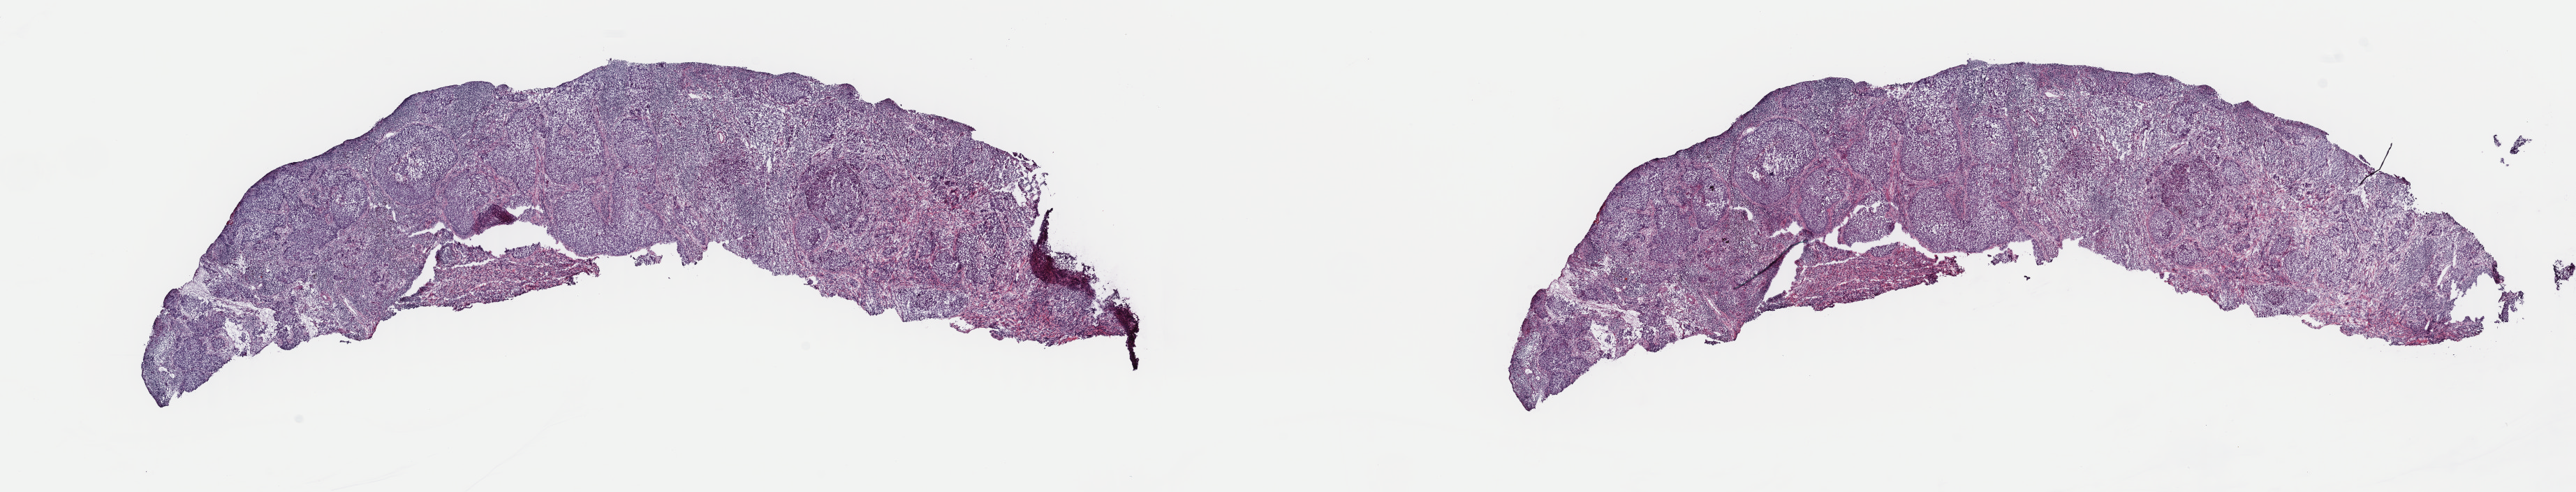
Digitized H&E tissue section (whole slide), whole scanned area (about 29.1 x 5.6 mm, from a 40x scan) shown as a low-resolution overview, frozen section from the top of the tissue portion, sample: primary tumour, lung. Patient: male, age at initial diagnosis 64 years. Pathologist review of this section (percent, as recorded): tumour cells 80%, tumour nuclei 80%, normal cells 0%, stromal cells 19%, necrosis 1%. Infiltration values recorded for this section: lymphocyte infiltration 4%, monocyte infiltration 1%, neutrophil infiltration 2%.
Diagnosis: Squamous cell carcinoma, NOS. AJCC pathologic stage: IIA. TNM: T2a N1 M0.